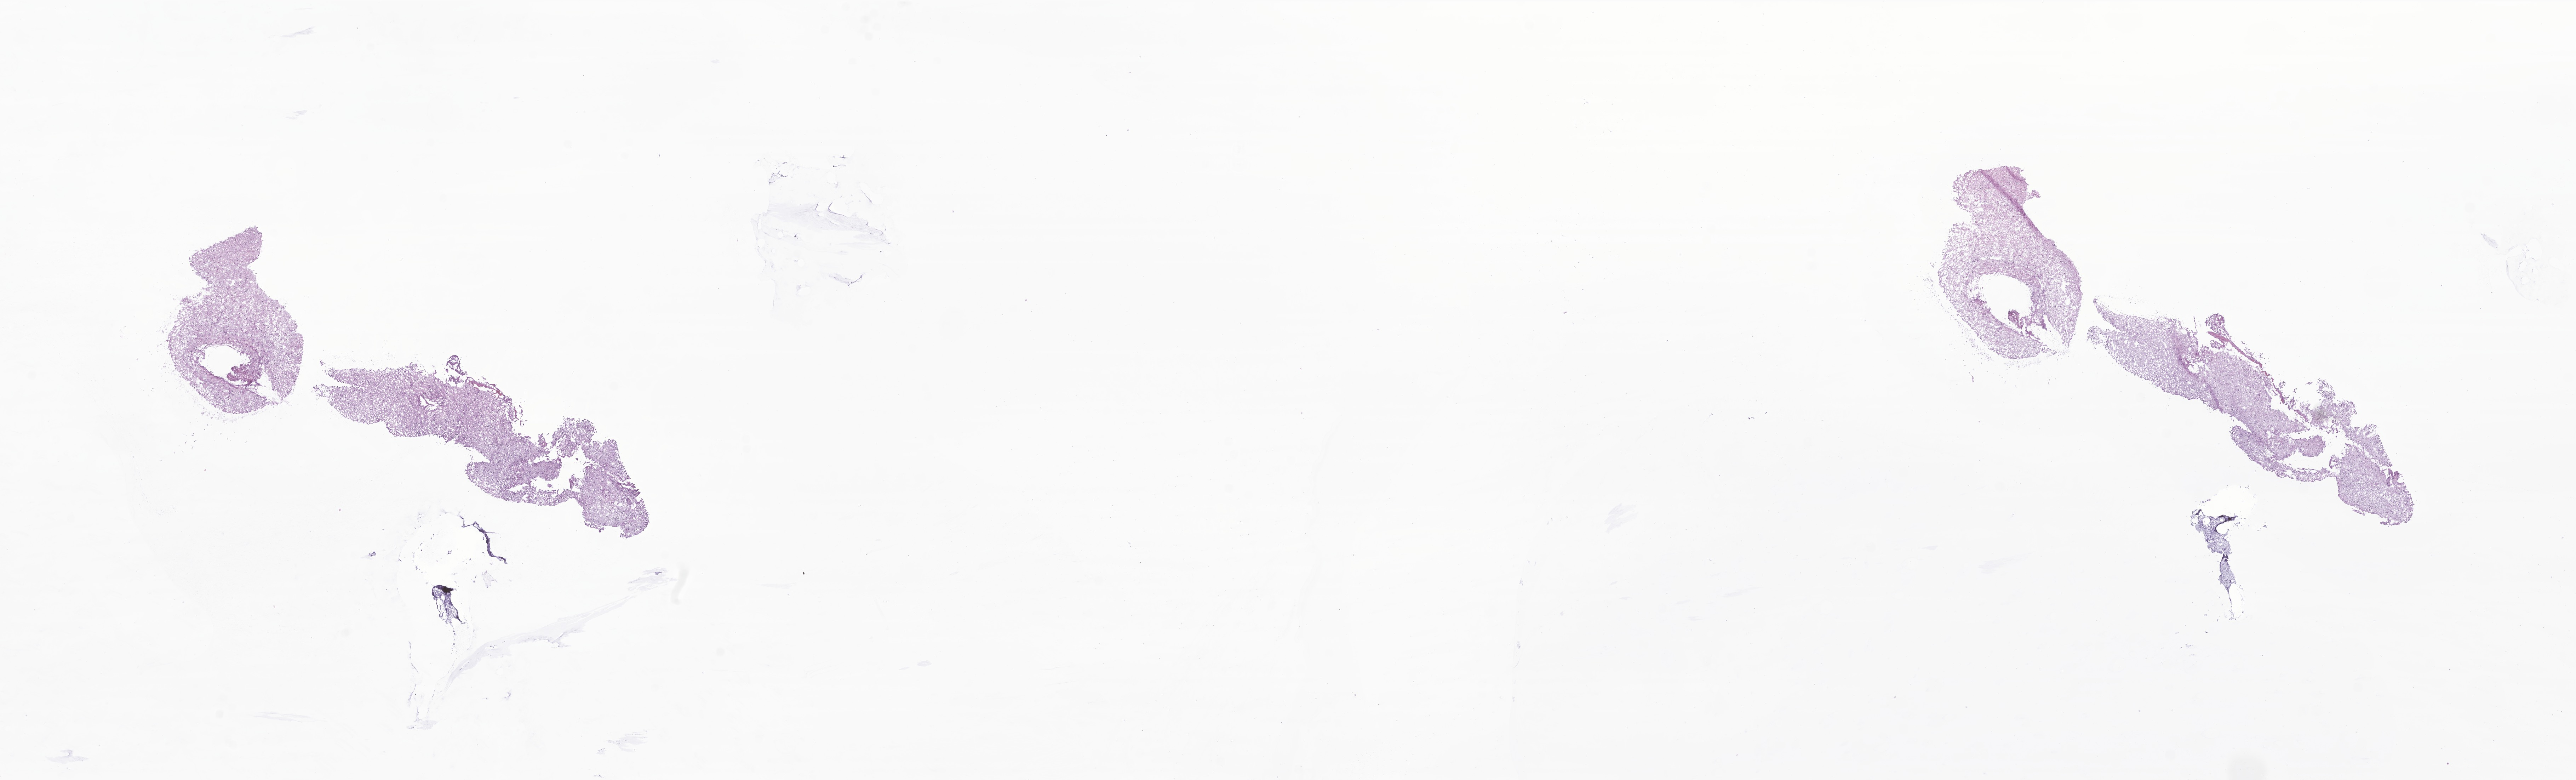
Digitized hematoxylin and eosin (H&E)-stained section of tumor tissue from the cerebral ventricle, a low-resolution overview of the entire scanned area, about 30.7 x 9.3 mm. Frozen section. Patient female; age 141 months (11 years 9 months).
• diagnosis (ICD-O-3 morphology term): Pilocytic astrocytoma